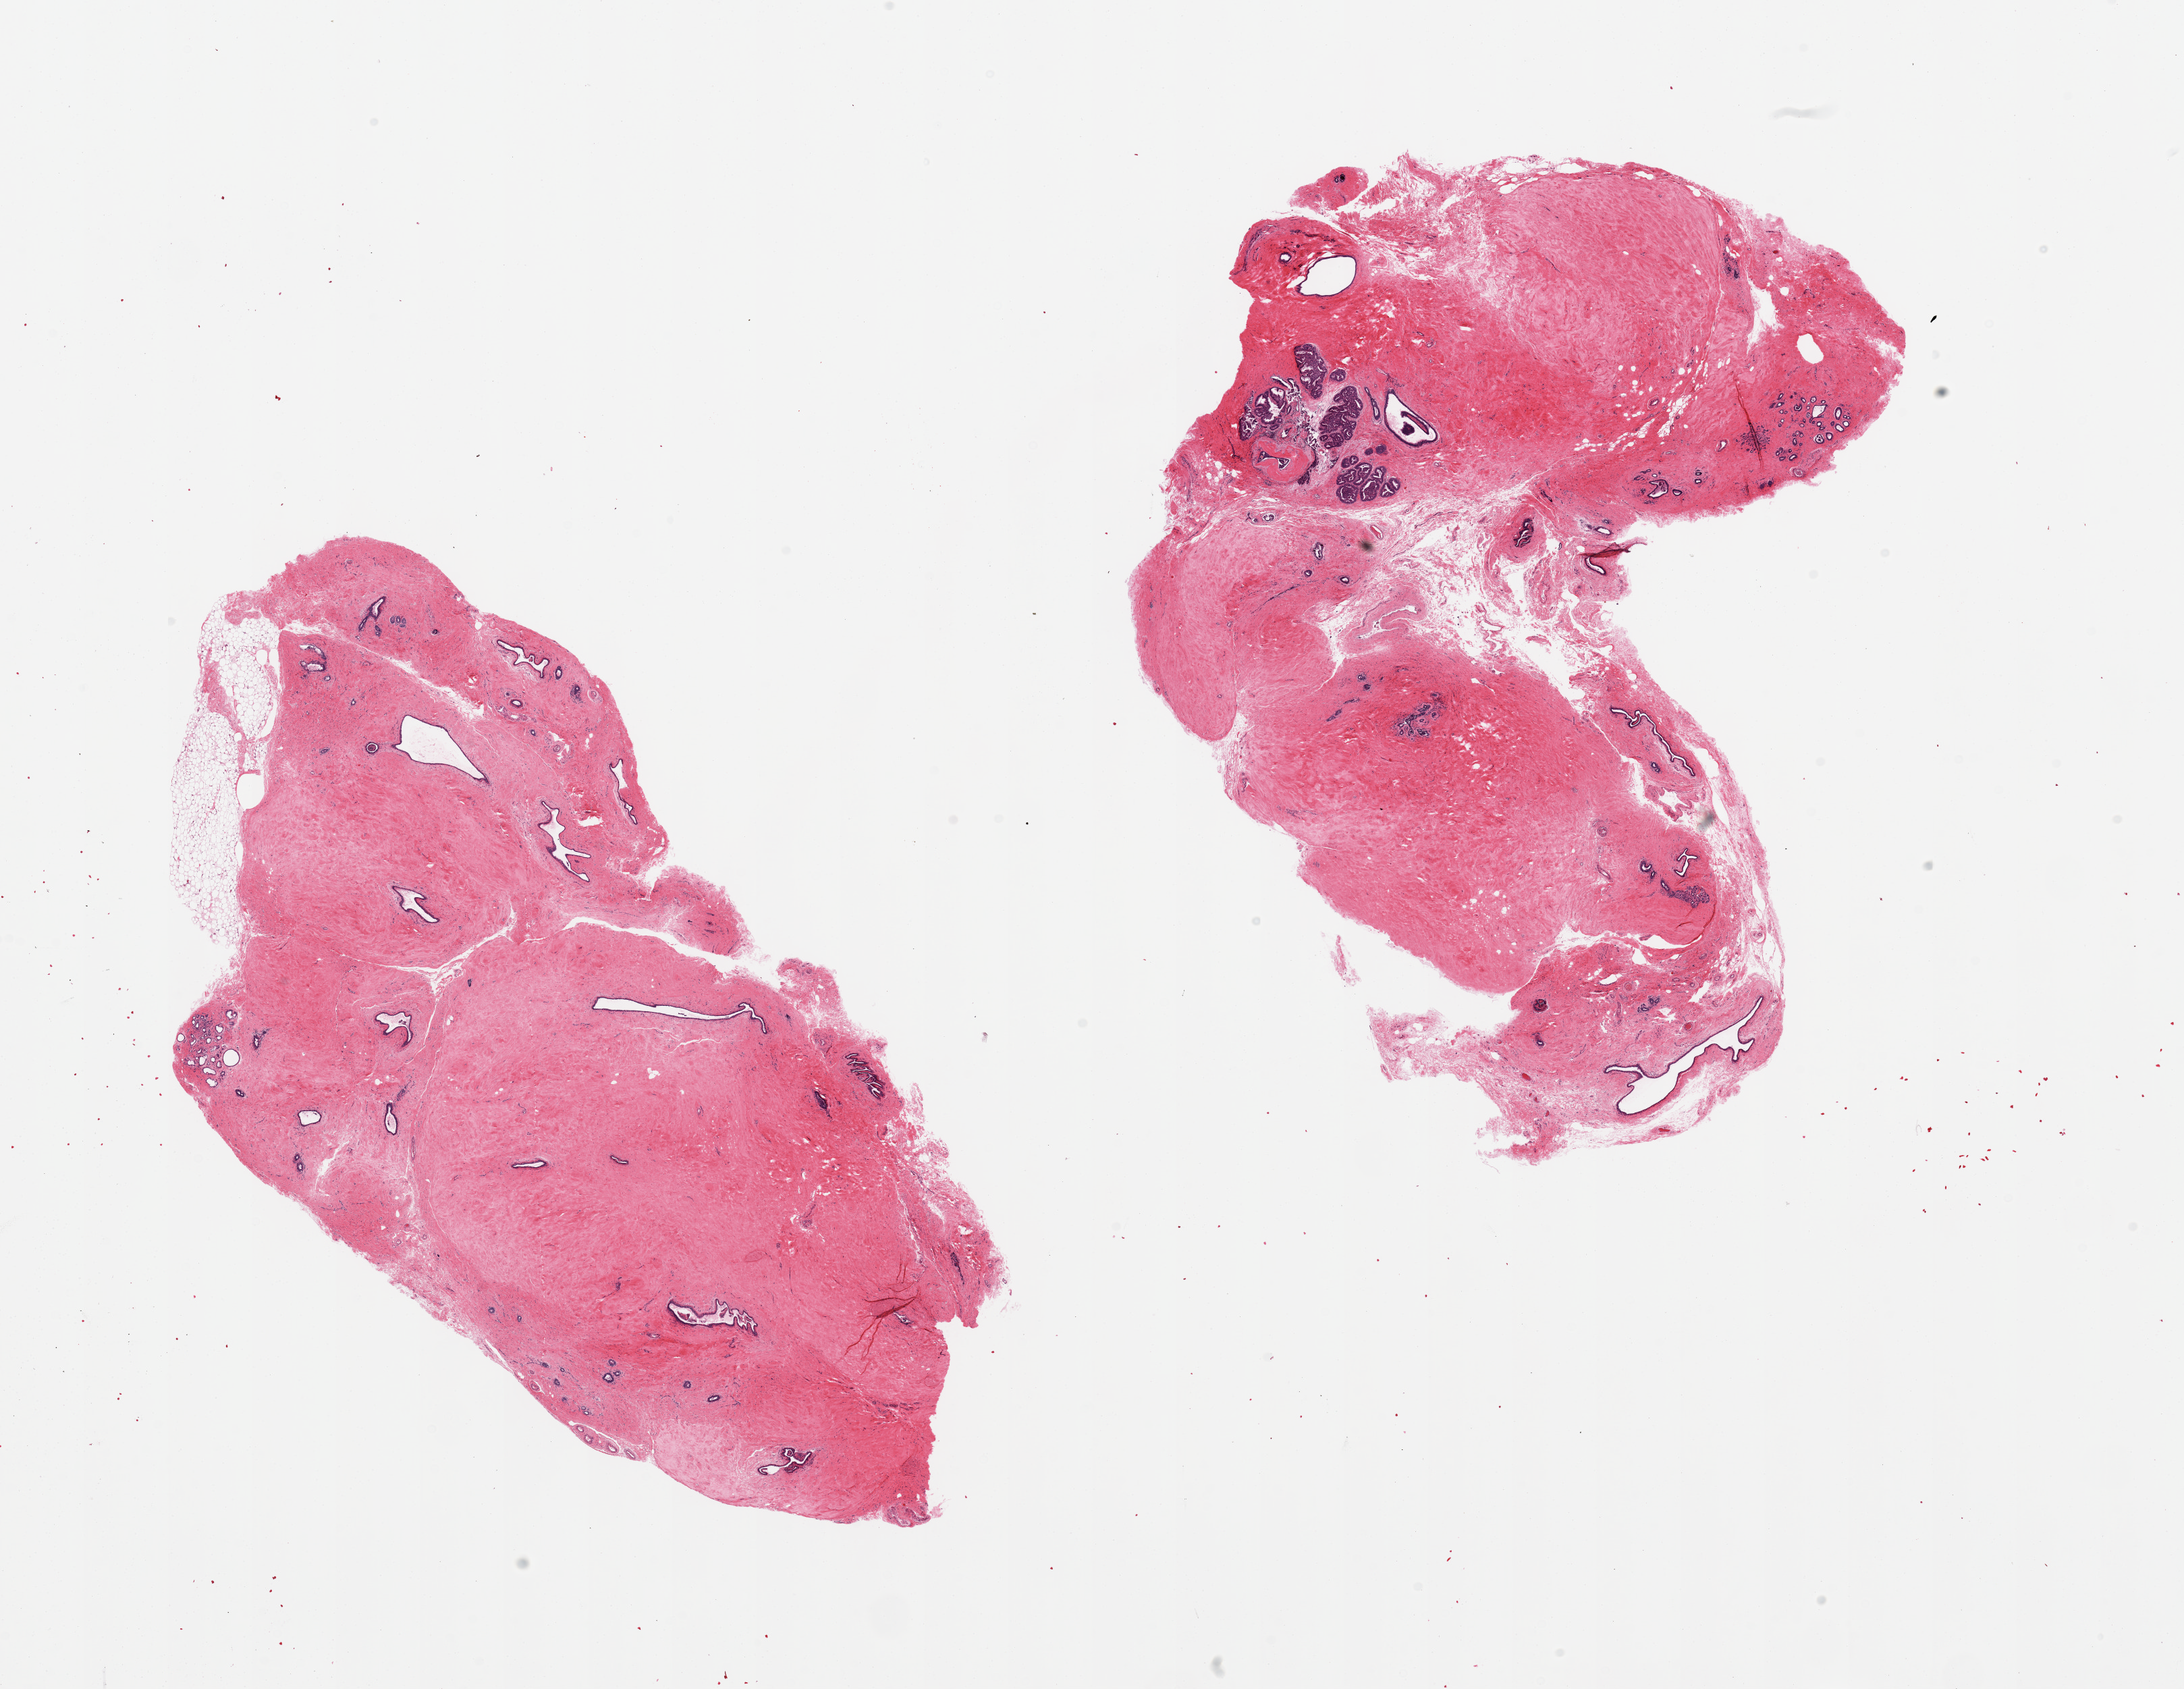
Hematoxylin and eosin (H&E) whole-slide image, whole scanned area (about 25.6 x 19.8 mm, acquisition: 20x scan) shown as a low-resolution overview; PAXgene-fixed paraffin-embedded (PFPE) section; target tissue: breast; donor tissue sample. Female donor.
• reviewer comment on this tissue sample: 2 pieces, fibrocystic change, prominent simple hyperplasia in one TDLU and, one section